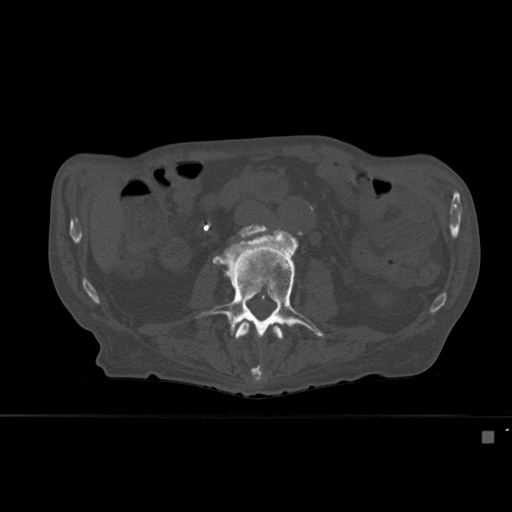
CT including the spine, one axial slice. Position 215 of 527 along the scan axis. Bone window (W 1800 / L 400 HU). 1.5 mm slice thickness. 512 × 512 image matrix, field of view 373 × 373 mm. Patient: male, 78 years. Case-level facts recorded for this patient, not image findings: primary cancer: prostate.
Outlined on this slice (semi-automatically segmented with operator editing):
- L2 vertebra: bounding box [x1, y1, x2, y2] px = [234, 320, 283, 383]
- L3 vertebra: [196, 227, 325, 373]
- L4 vertebra: [239, 227, 268, 238]